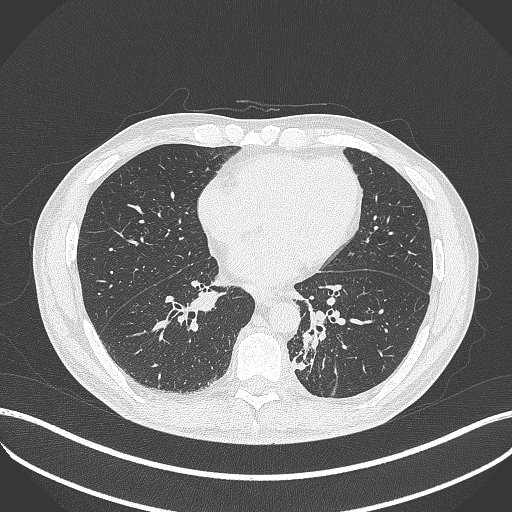
Chest CT, one axial slice; position 159 of 451 along the scan axis; reconstruction kernel B70f; 120 kVp; lung window (W 1500 / L -600 HU); 1 mm slice thickness; 512 × 512 image matrix. Patient: male, 72 years. From the clinical record (not read from this slice): clinical TNM (as recorded): T2b N0 M1.
Structures marked on this image (rectangle marked by the reading radiologist):
- lung tumour (recorded histology: adenocarcinoma): box from (x=291, y=328) to (x=323, y=372) px